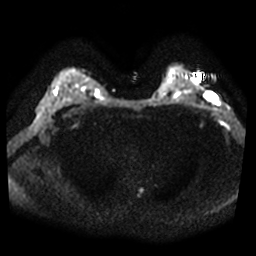
Breast MRI, one axial slice; slice 31 of 38 in the series (ordered by position); diffusion-weighted series; image 2 of 4 stored at this slice position (different b-values; order by instance number); 3 T; 5 mm slice thickness; 256 × 256 image matrix. Female patient.
Structures marked on this image (expert manual segmentation):
- tumour on diffusion-weighted imaging: bounding box (x1, y1, x2, y2) in pixels: (208, 92, 218, 103)